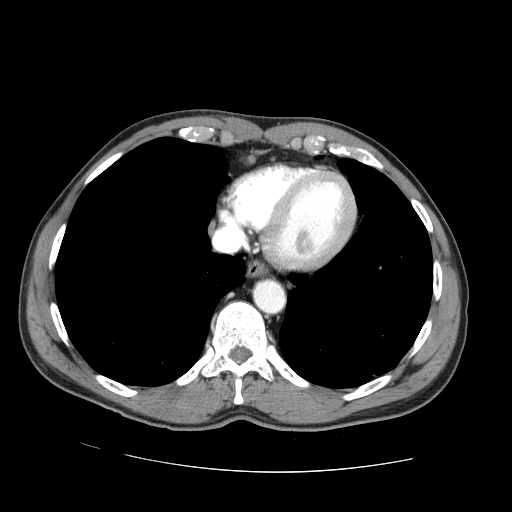
Contrast-enhanced abdominal CT (liver protocol), one axial slice. Slice 69 of 73 in the series (ordered by position). Reconstruction kernel STANDARD. 100 kVp. One of 2 acquisitions stored at this slice position. Soft-tissue window (W 400 / L 40 HU). 2.5 mm slice thickness. 512 × 512 image matrix, field of view 380 × 380 mm. Case-level facts recorded for this patient, not image findings: diagnosis: hepatocellular carcinoma (patient treated with transarterial chemoembolisation; whether this scan precedes or follows treatment is not stated here); TNM stage (as recorded): Stage-IVA; Child-Pugh class: A; tumour differentiation: no biopsy.
Structures marked on this image (semi-automatically segmented with operator editing):
- abdominal aorta: bounding box <254,281,284,312> (left, top, right, bottom; pixels)